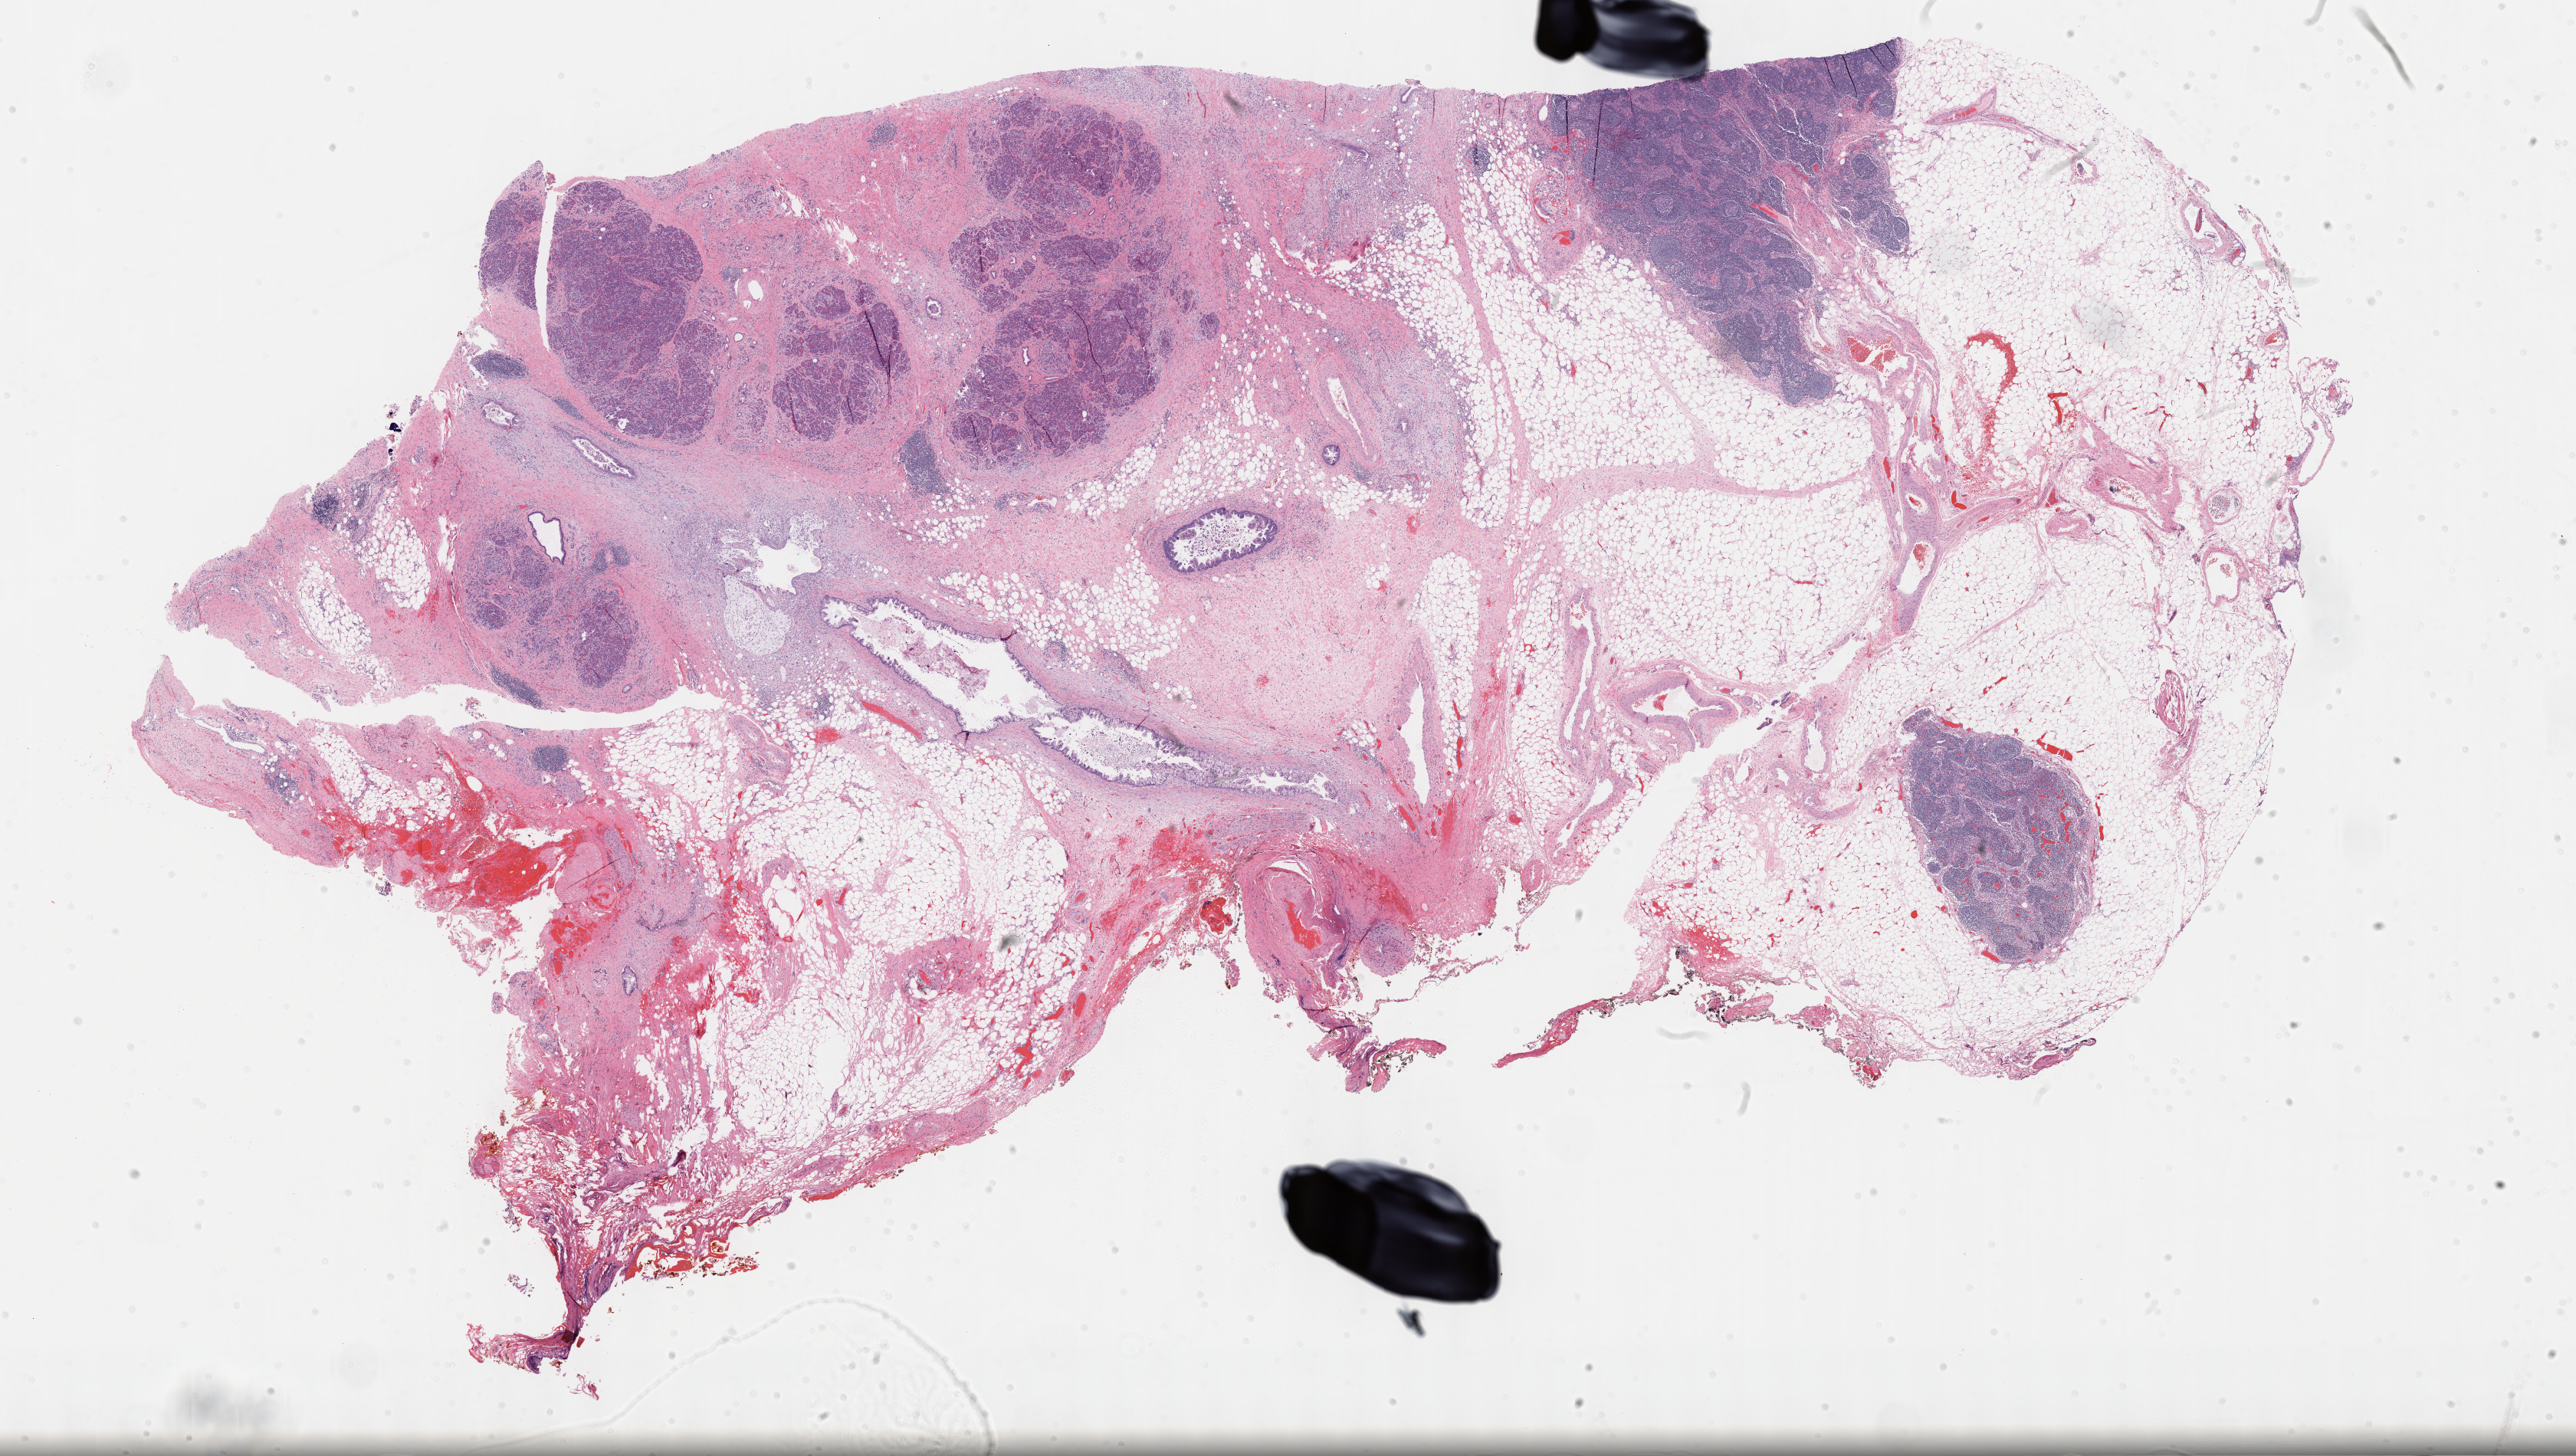
Digitized Hematoxylin and eosin (H&E) stained tissue section (whole slide), whole scanned area (about 27.2 x 15.4 mm, acquisition: 40x scan) shown as a low-resolution overview; FFPE section; pancreas, primary tumour sample. Female, age 50 years at initial diagnosis. Histologic grade: G2 (moderately differentiated).
- histologic diagnosis: Infiltrating duct carcinoma, NOS (head of pancreas)
- AJCC pathologic stage: IIB (7th edition)
- lymph nodes positive (case pathology): 10 of 33 examined